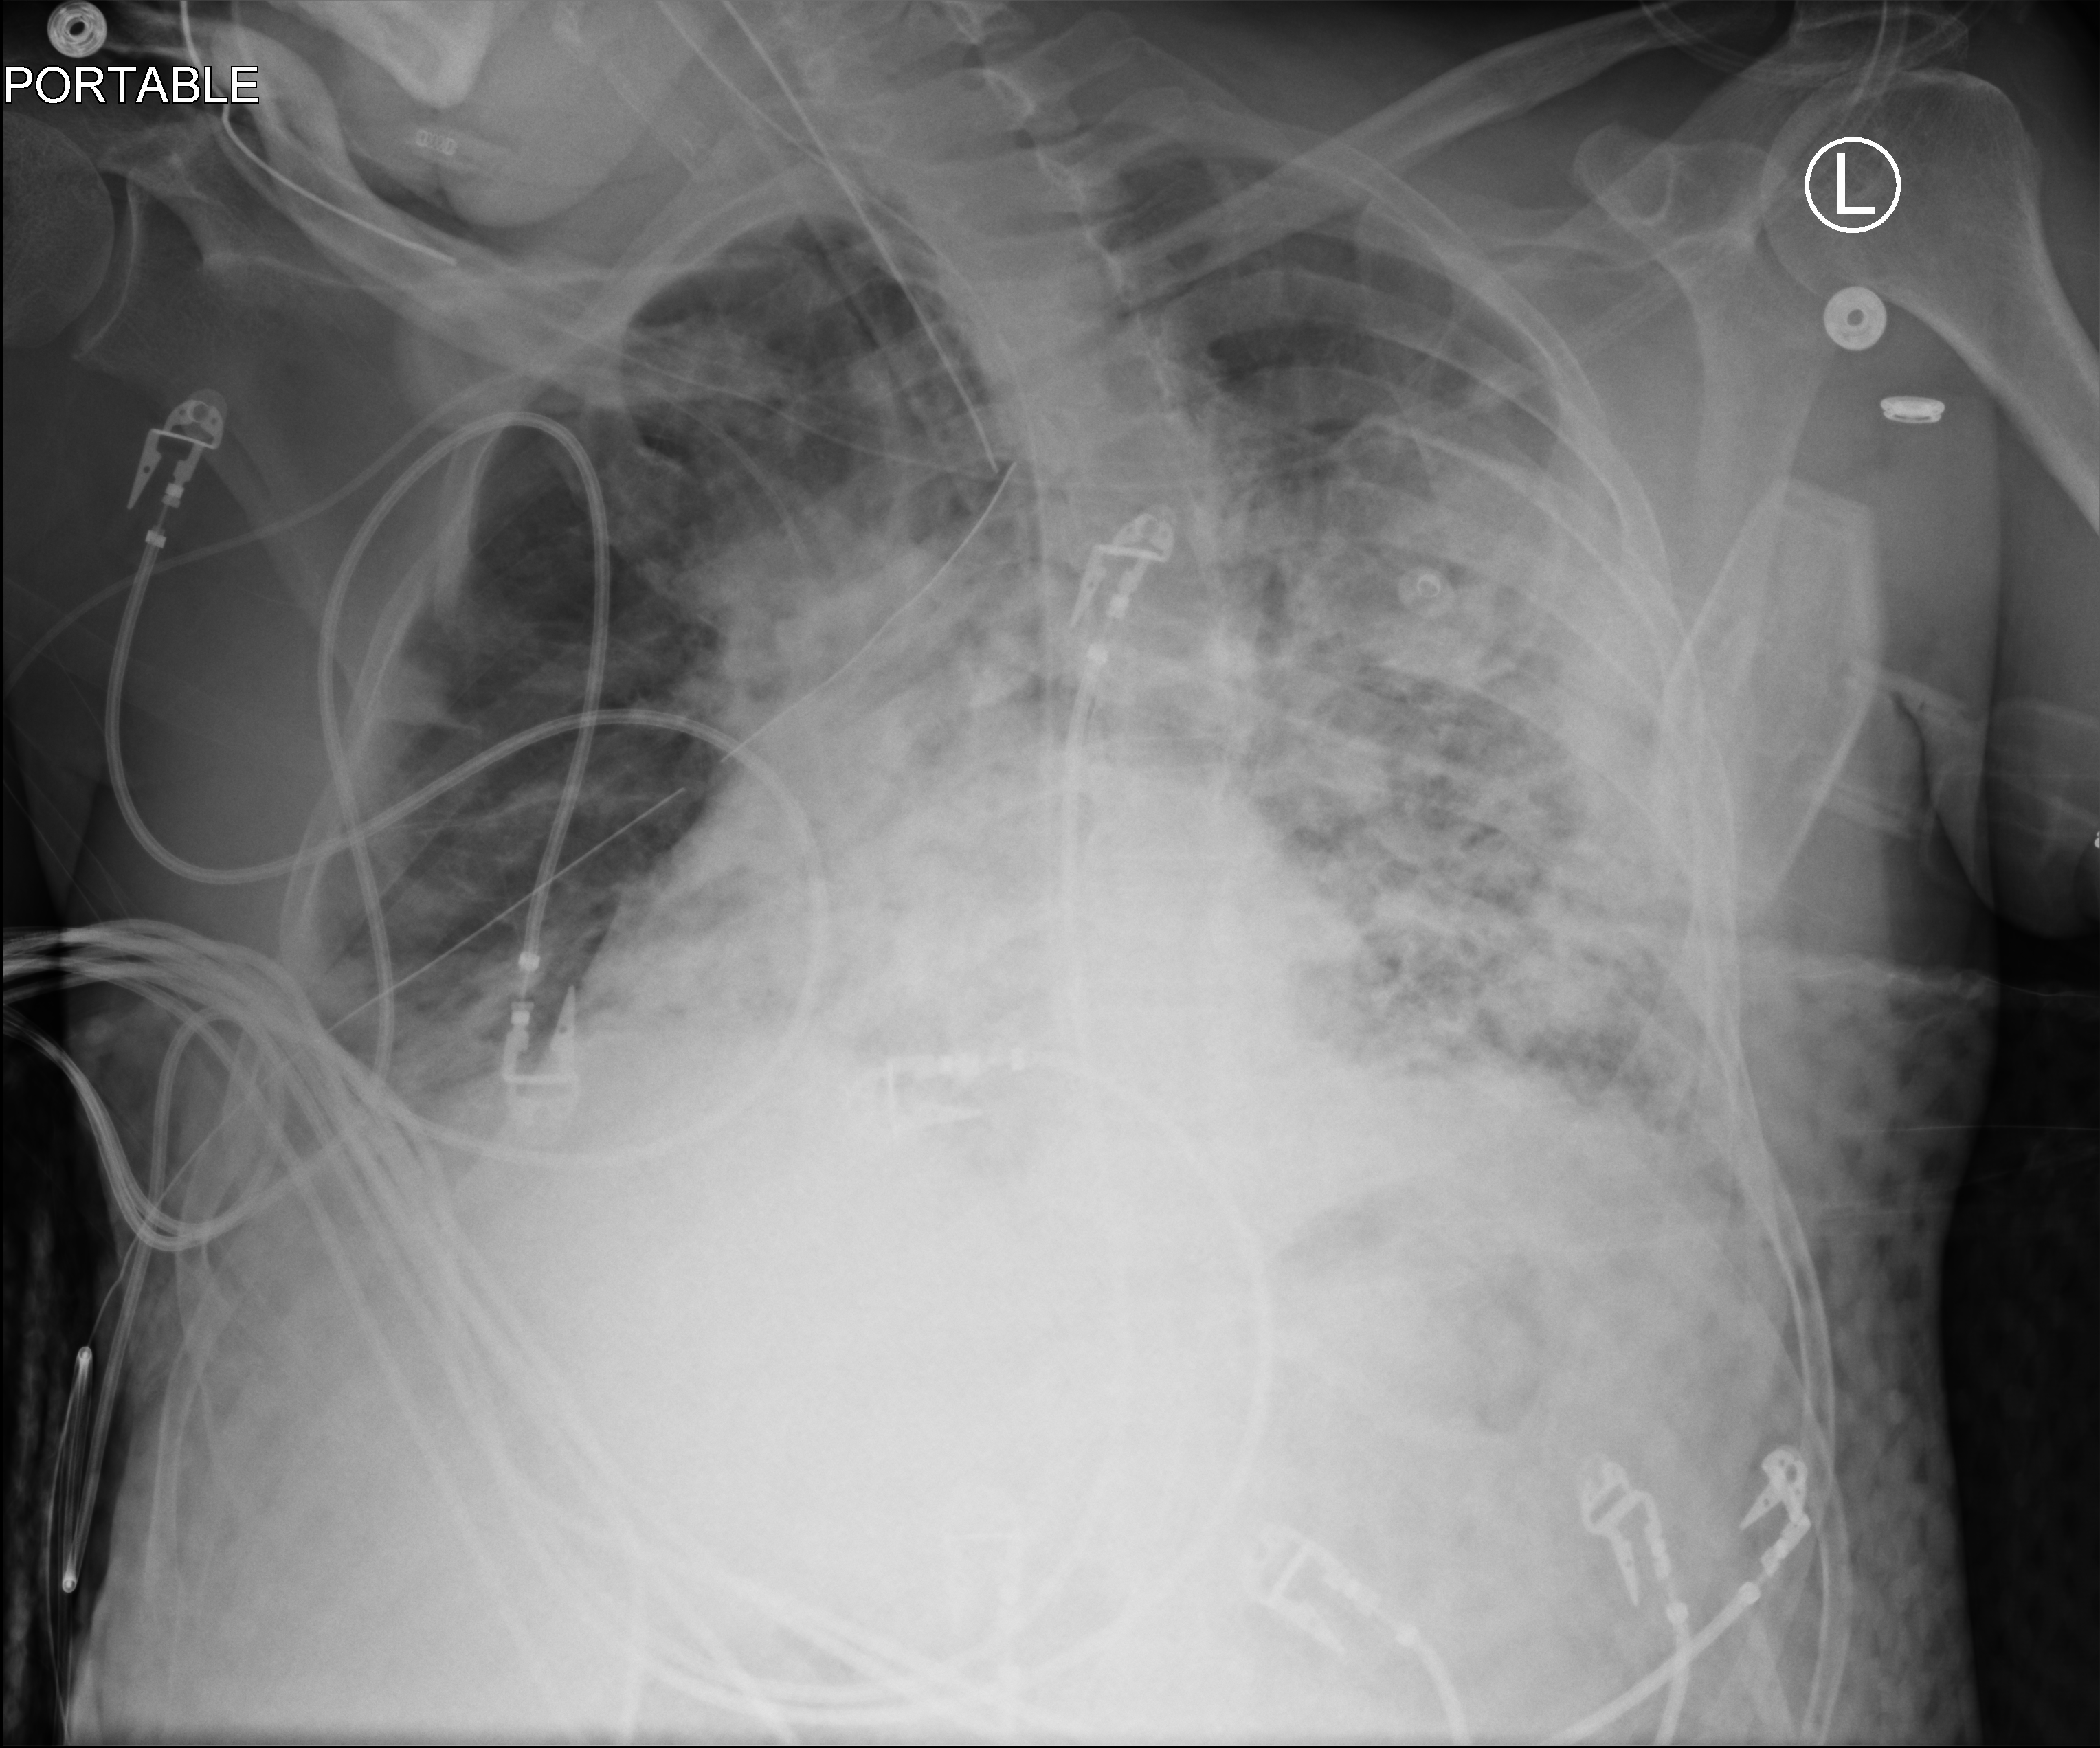
Portable chest radiograph; anteroposterior (AP) projection. Patient hospitalised with COVID-19; male, aged 18–59 years.
From the hospital-stay record, not from the radiograph (when in the stay this image was taken is not recorded): length of hospital stay: 41 days.